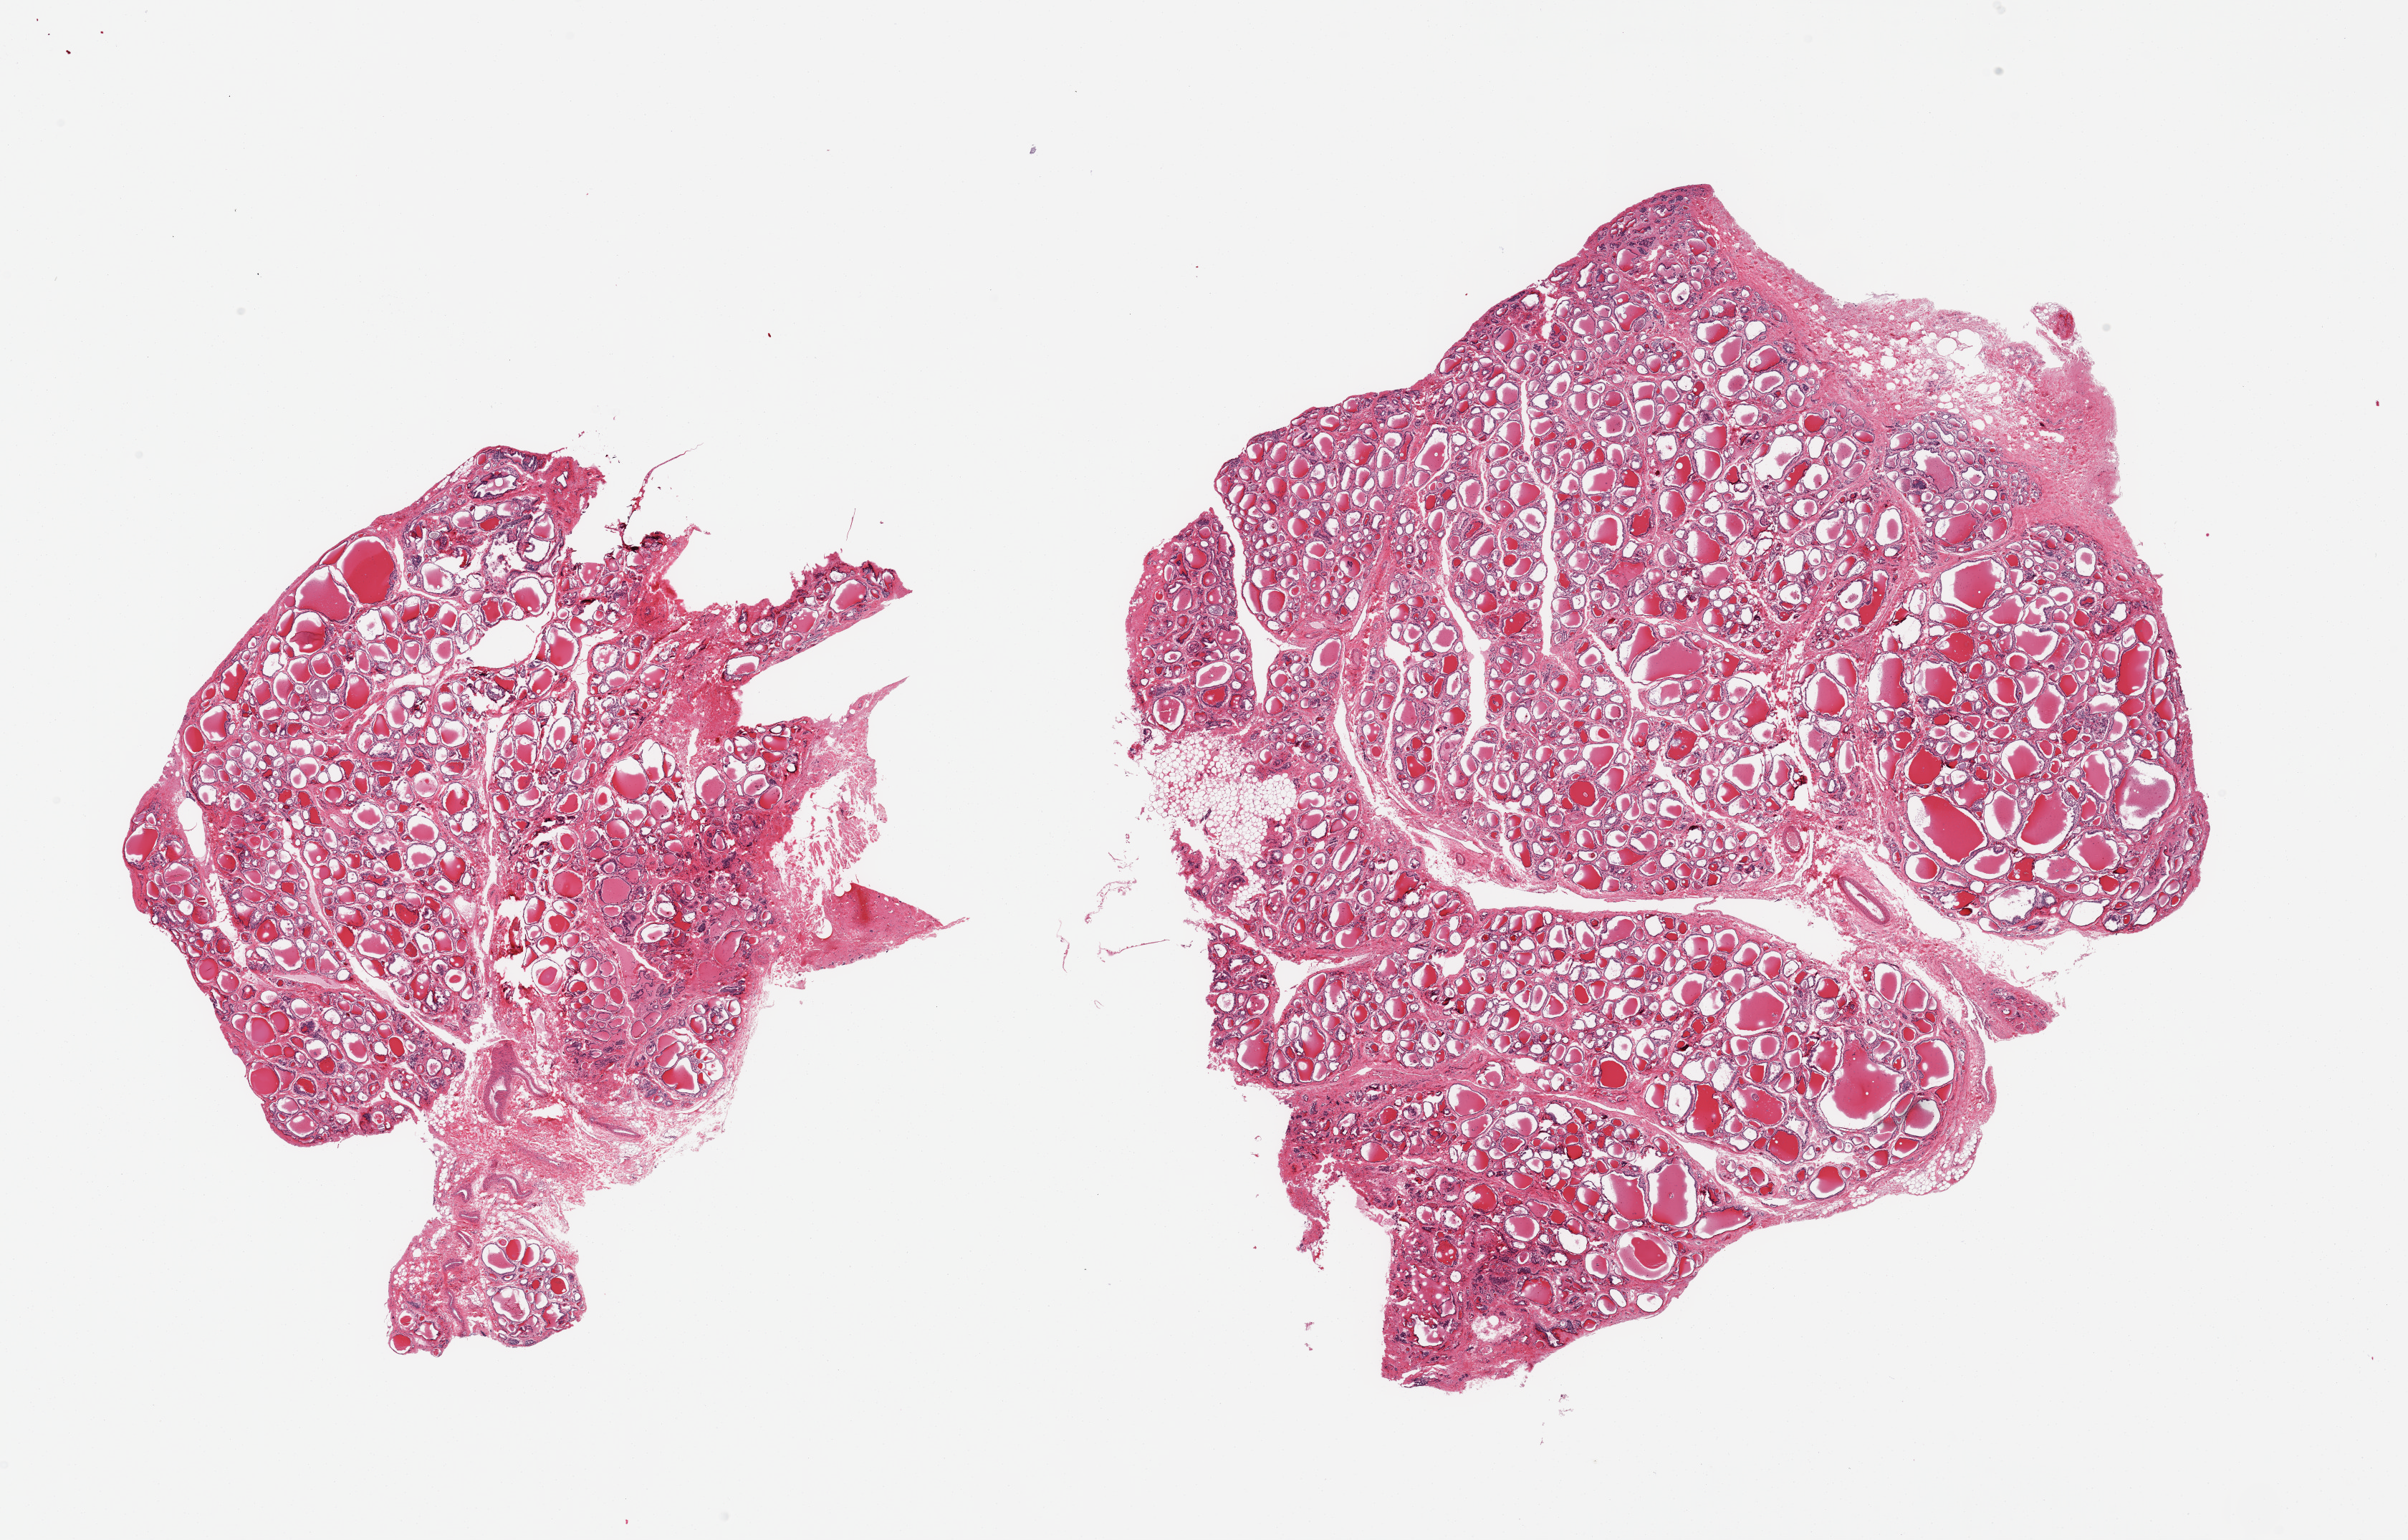
Whole-slide image, hematoxylin and eosin (H&E) stain, brightfield — a low-resolution overview of the entire scanned area, about 26.6 x 17.0 mm (slide scanned at 20x); PAXgene-fixed paraffin-embedded (PFPE) section; section of thyroid (target tissue); donor tissue sample. Donor sex: male.
Reviewer comment on this tissue sample: 2 pieces, mild goitrous features; ~1mm nubbin of adherent fat.